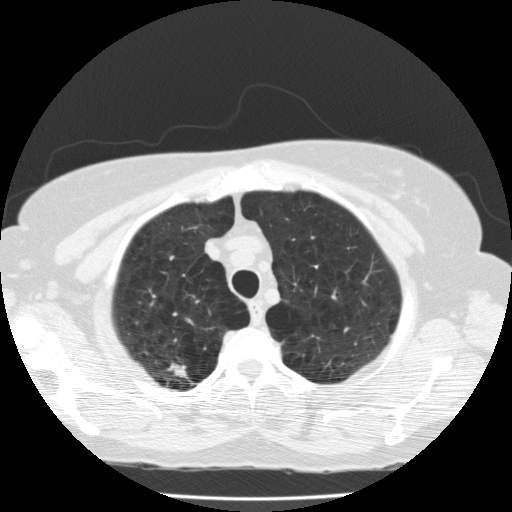
Axial slice from a low-dose chest CT screening exam. Second annual screen. Lung window (W 1500 / L -600 HU). Slice 29 of 174 in the series. Female participant, aged 59 years at enrolment. Current smoker at enrolment.
Expert reader's lesion annotation, bounding box <146,354,205,397> (left, top, right, bottom; pixels). The exam's reader record, not a measurement of the box and not confirmed to be the same lesion: non-calcified nodule or mass ≥4 mm, right upper lobe, 11 × 6 mm, spiculated (stellate) margins, soft tissue attenuation, pre-existing on the prior screen: yes; interval growth: no.